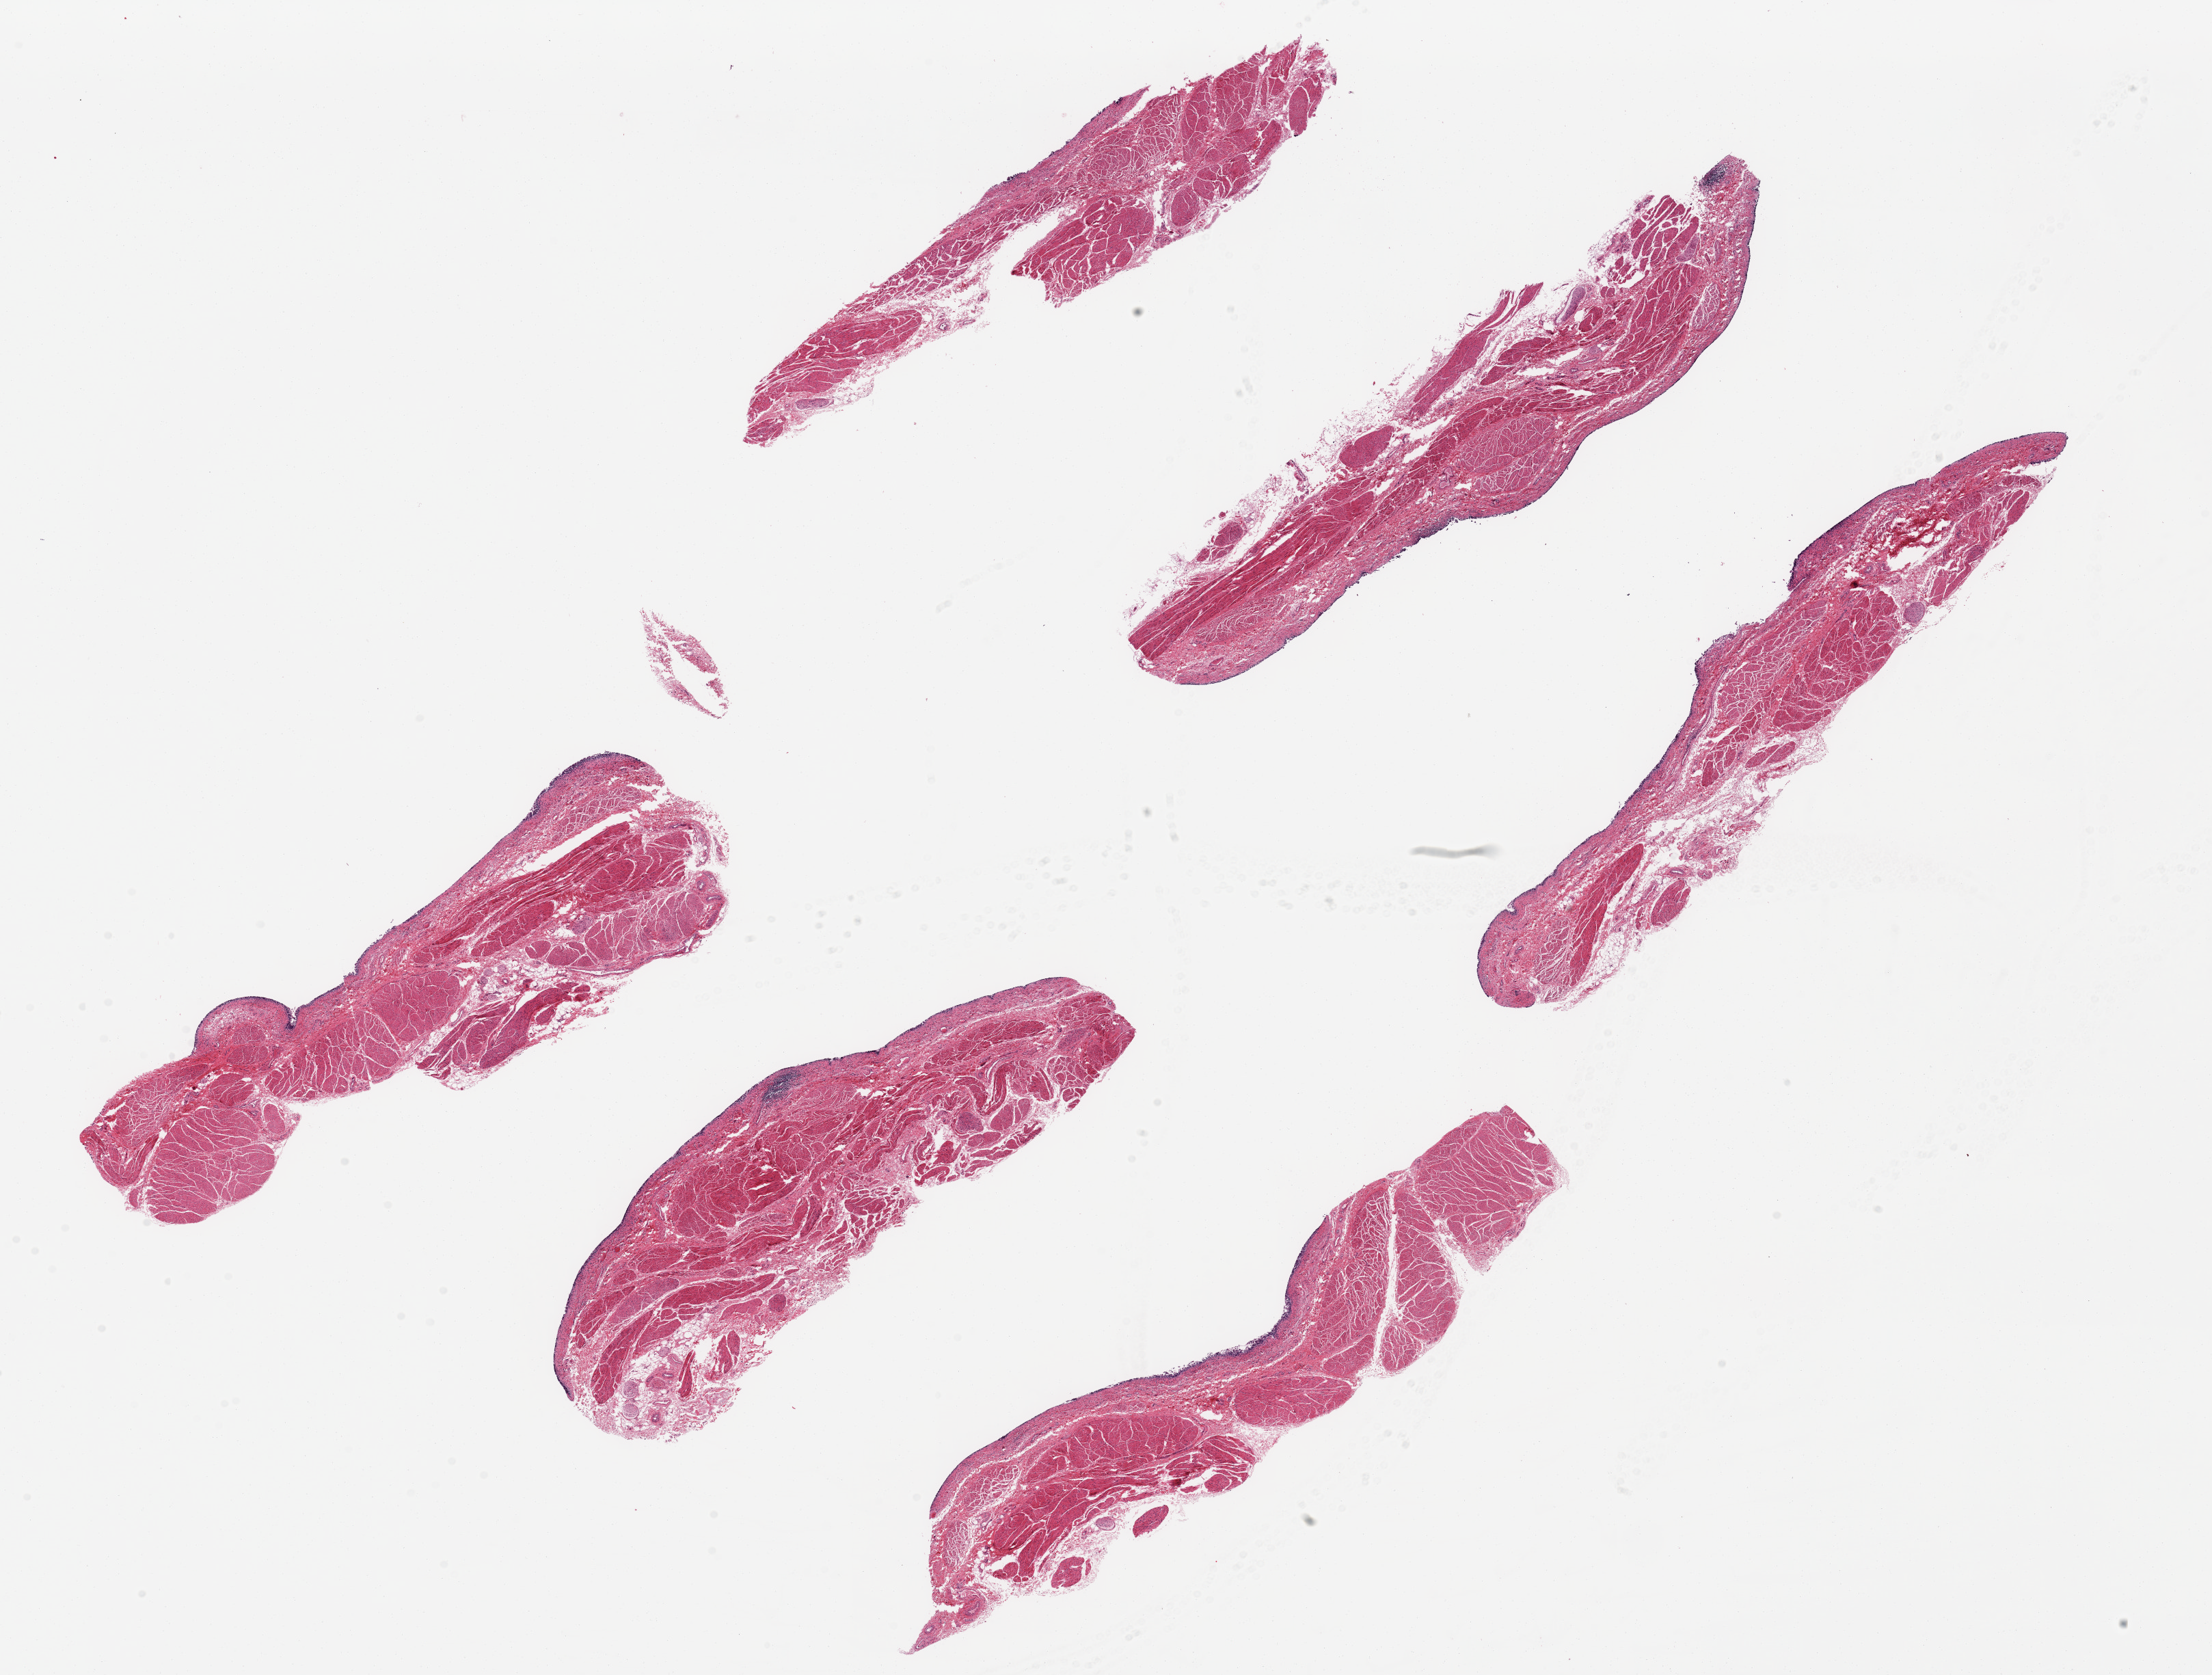
Digitized haematoxylin and eosin-stained section, low-resolution overview of the scanned area, about 25.6 x 19.4 mm (slide scanned at 20x); PAXgene-fixed paraffin-embedded (PFPE) section; target tissue: urinary bladder; tissue donor sample. Donor: female.
- review note (as recorded): 3 epi, 1 wall, 6 ~9x2 mm pieces. Almost totally sloughed epithelium